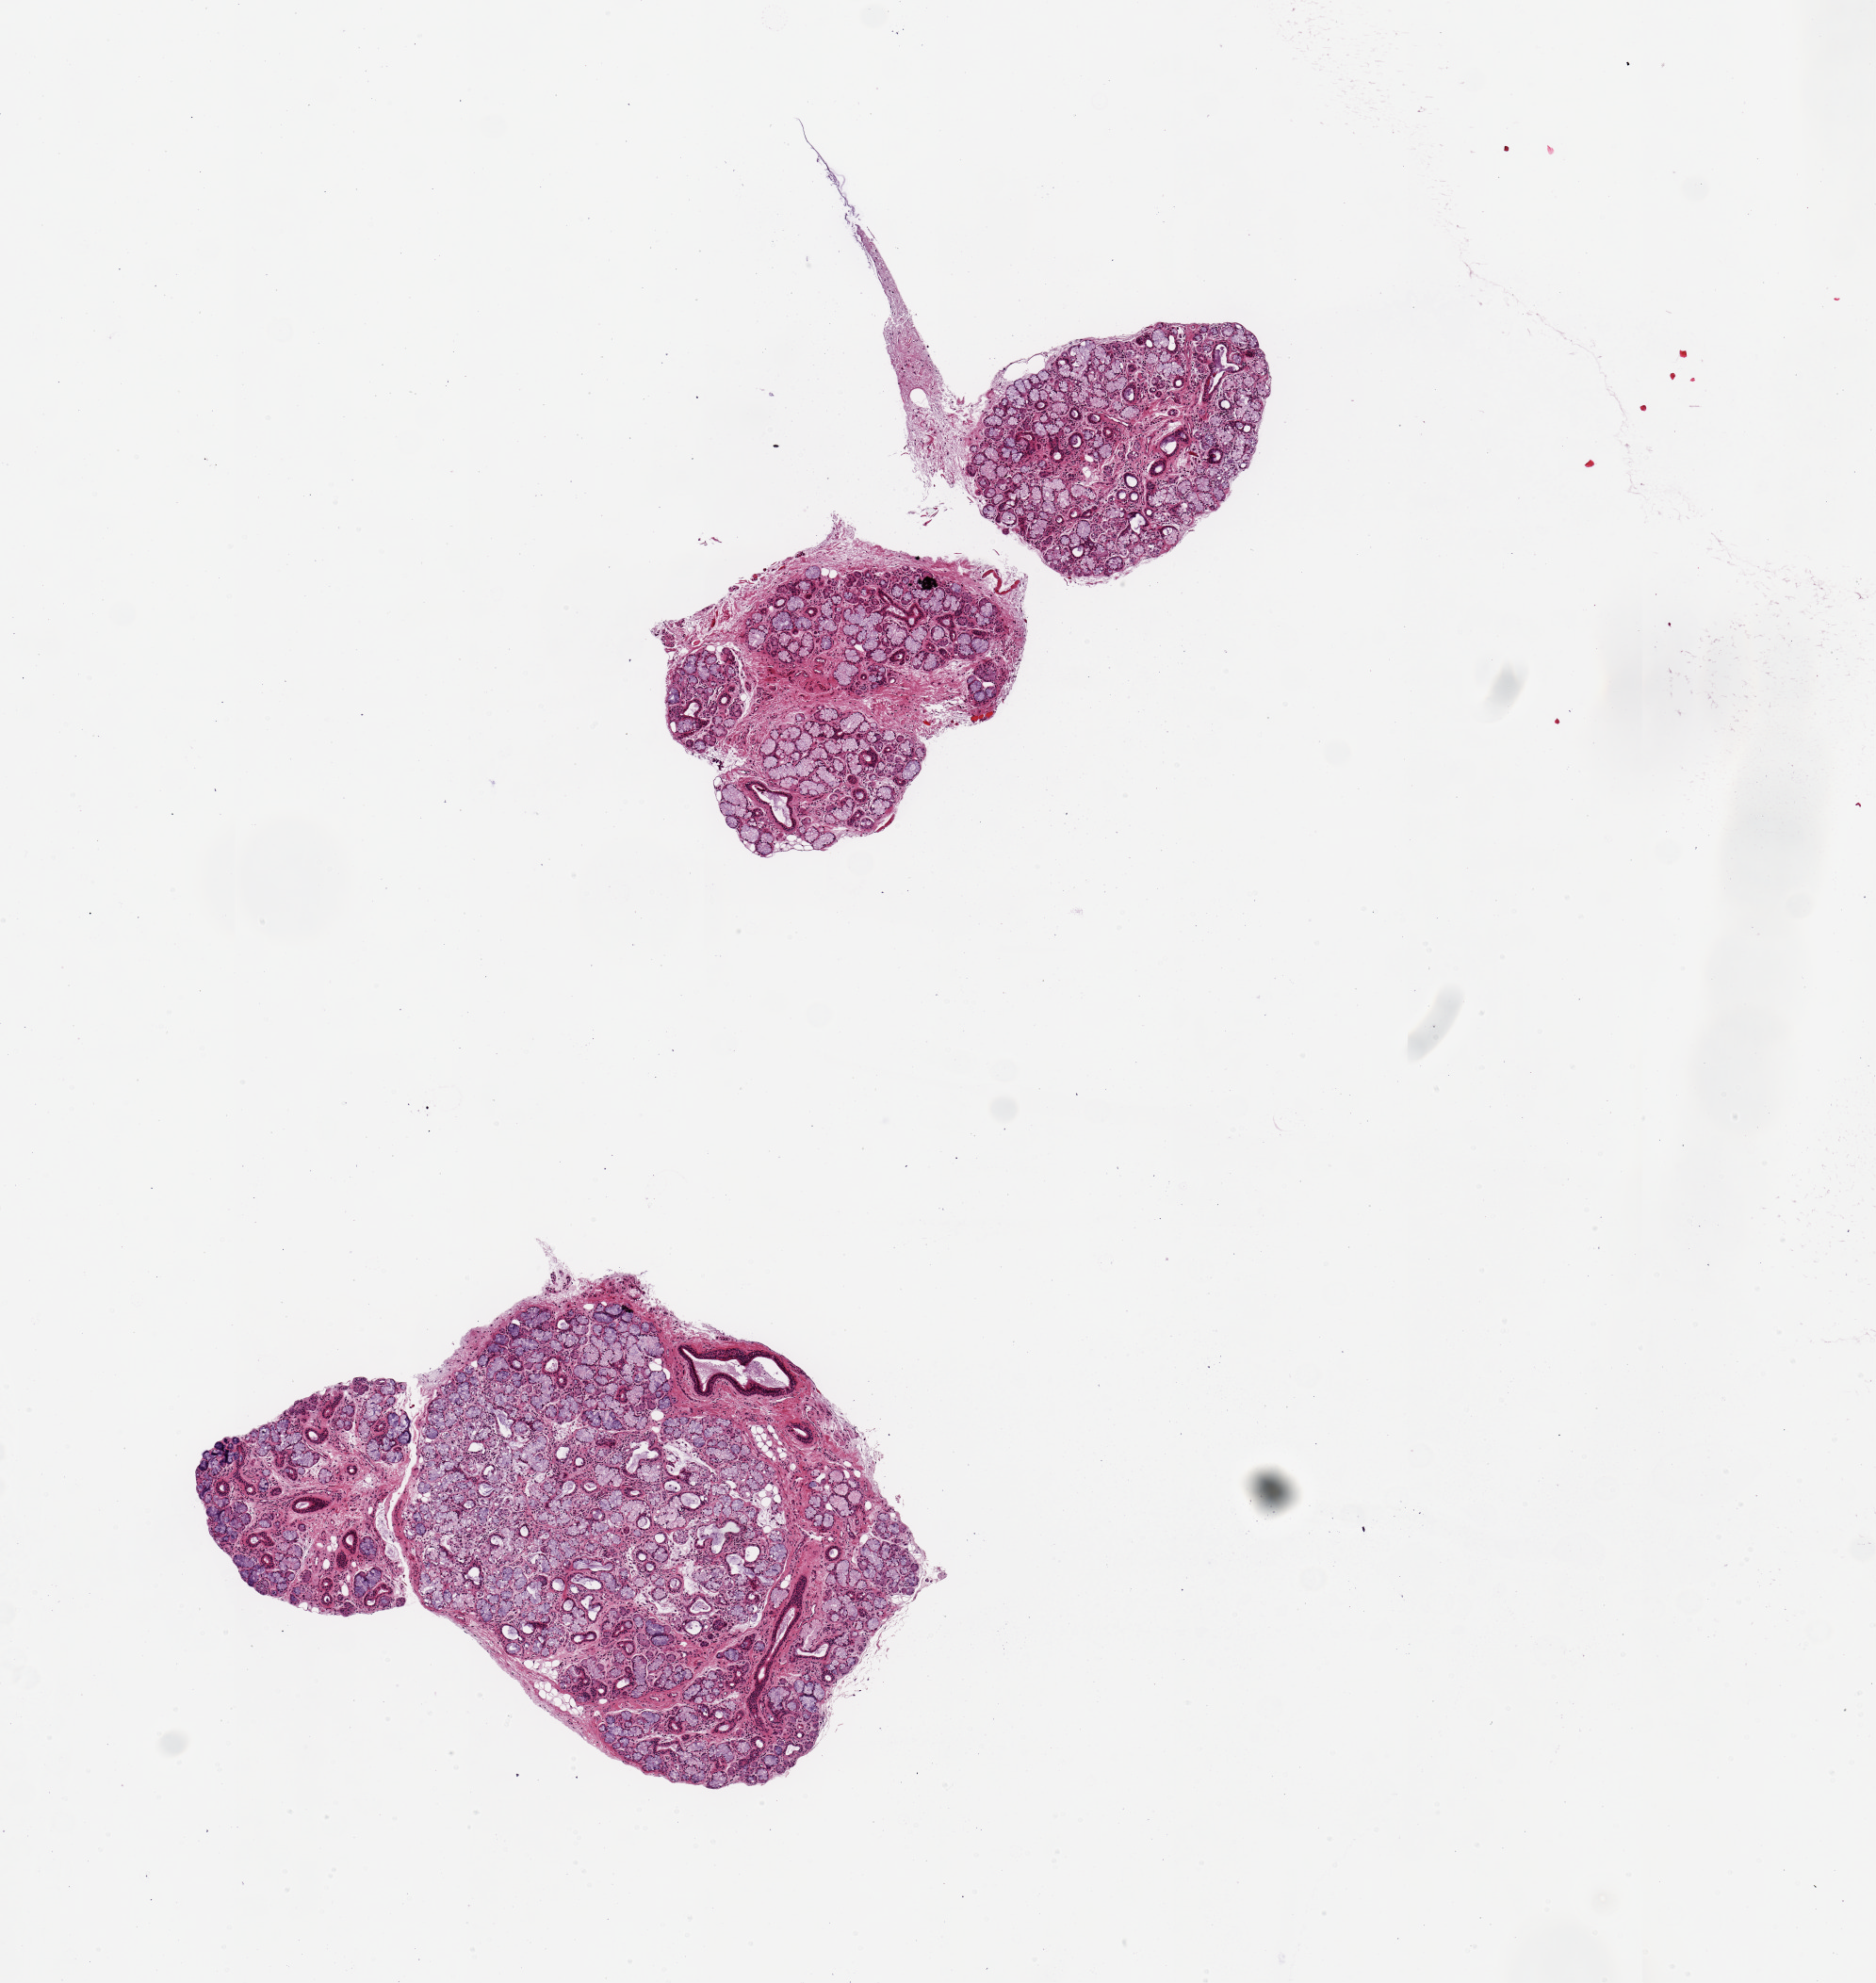
Haematoxylin and eosin whole-slide image, brightfield — low-resolution overview of the scanned area, about 7.9 x 8.3 mm. PAXgene-fixed, paraffin-embedded tissue. Target tissue: minor salivary gland. Tissue donor sample. Male donor.
Reviewer comment on this tissue sample: 3 pieces ~1.5; Glands and ductules noted (representative ducts).